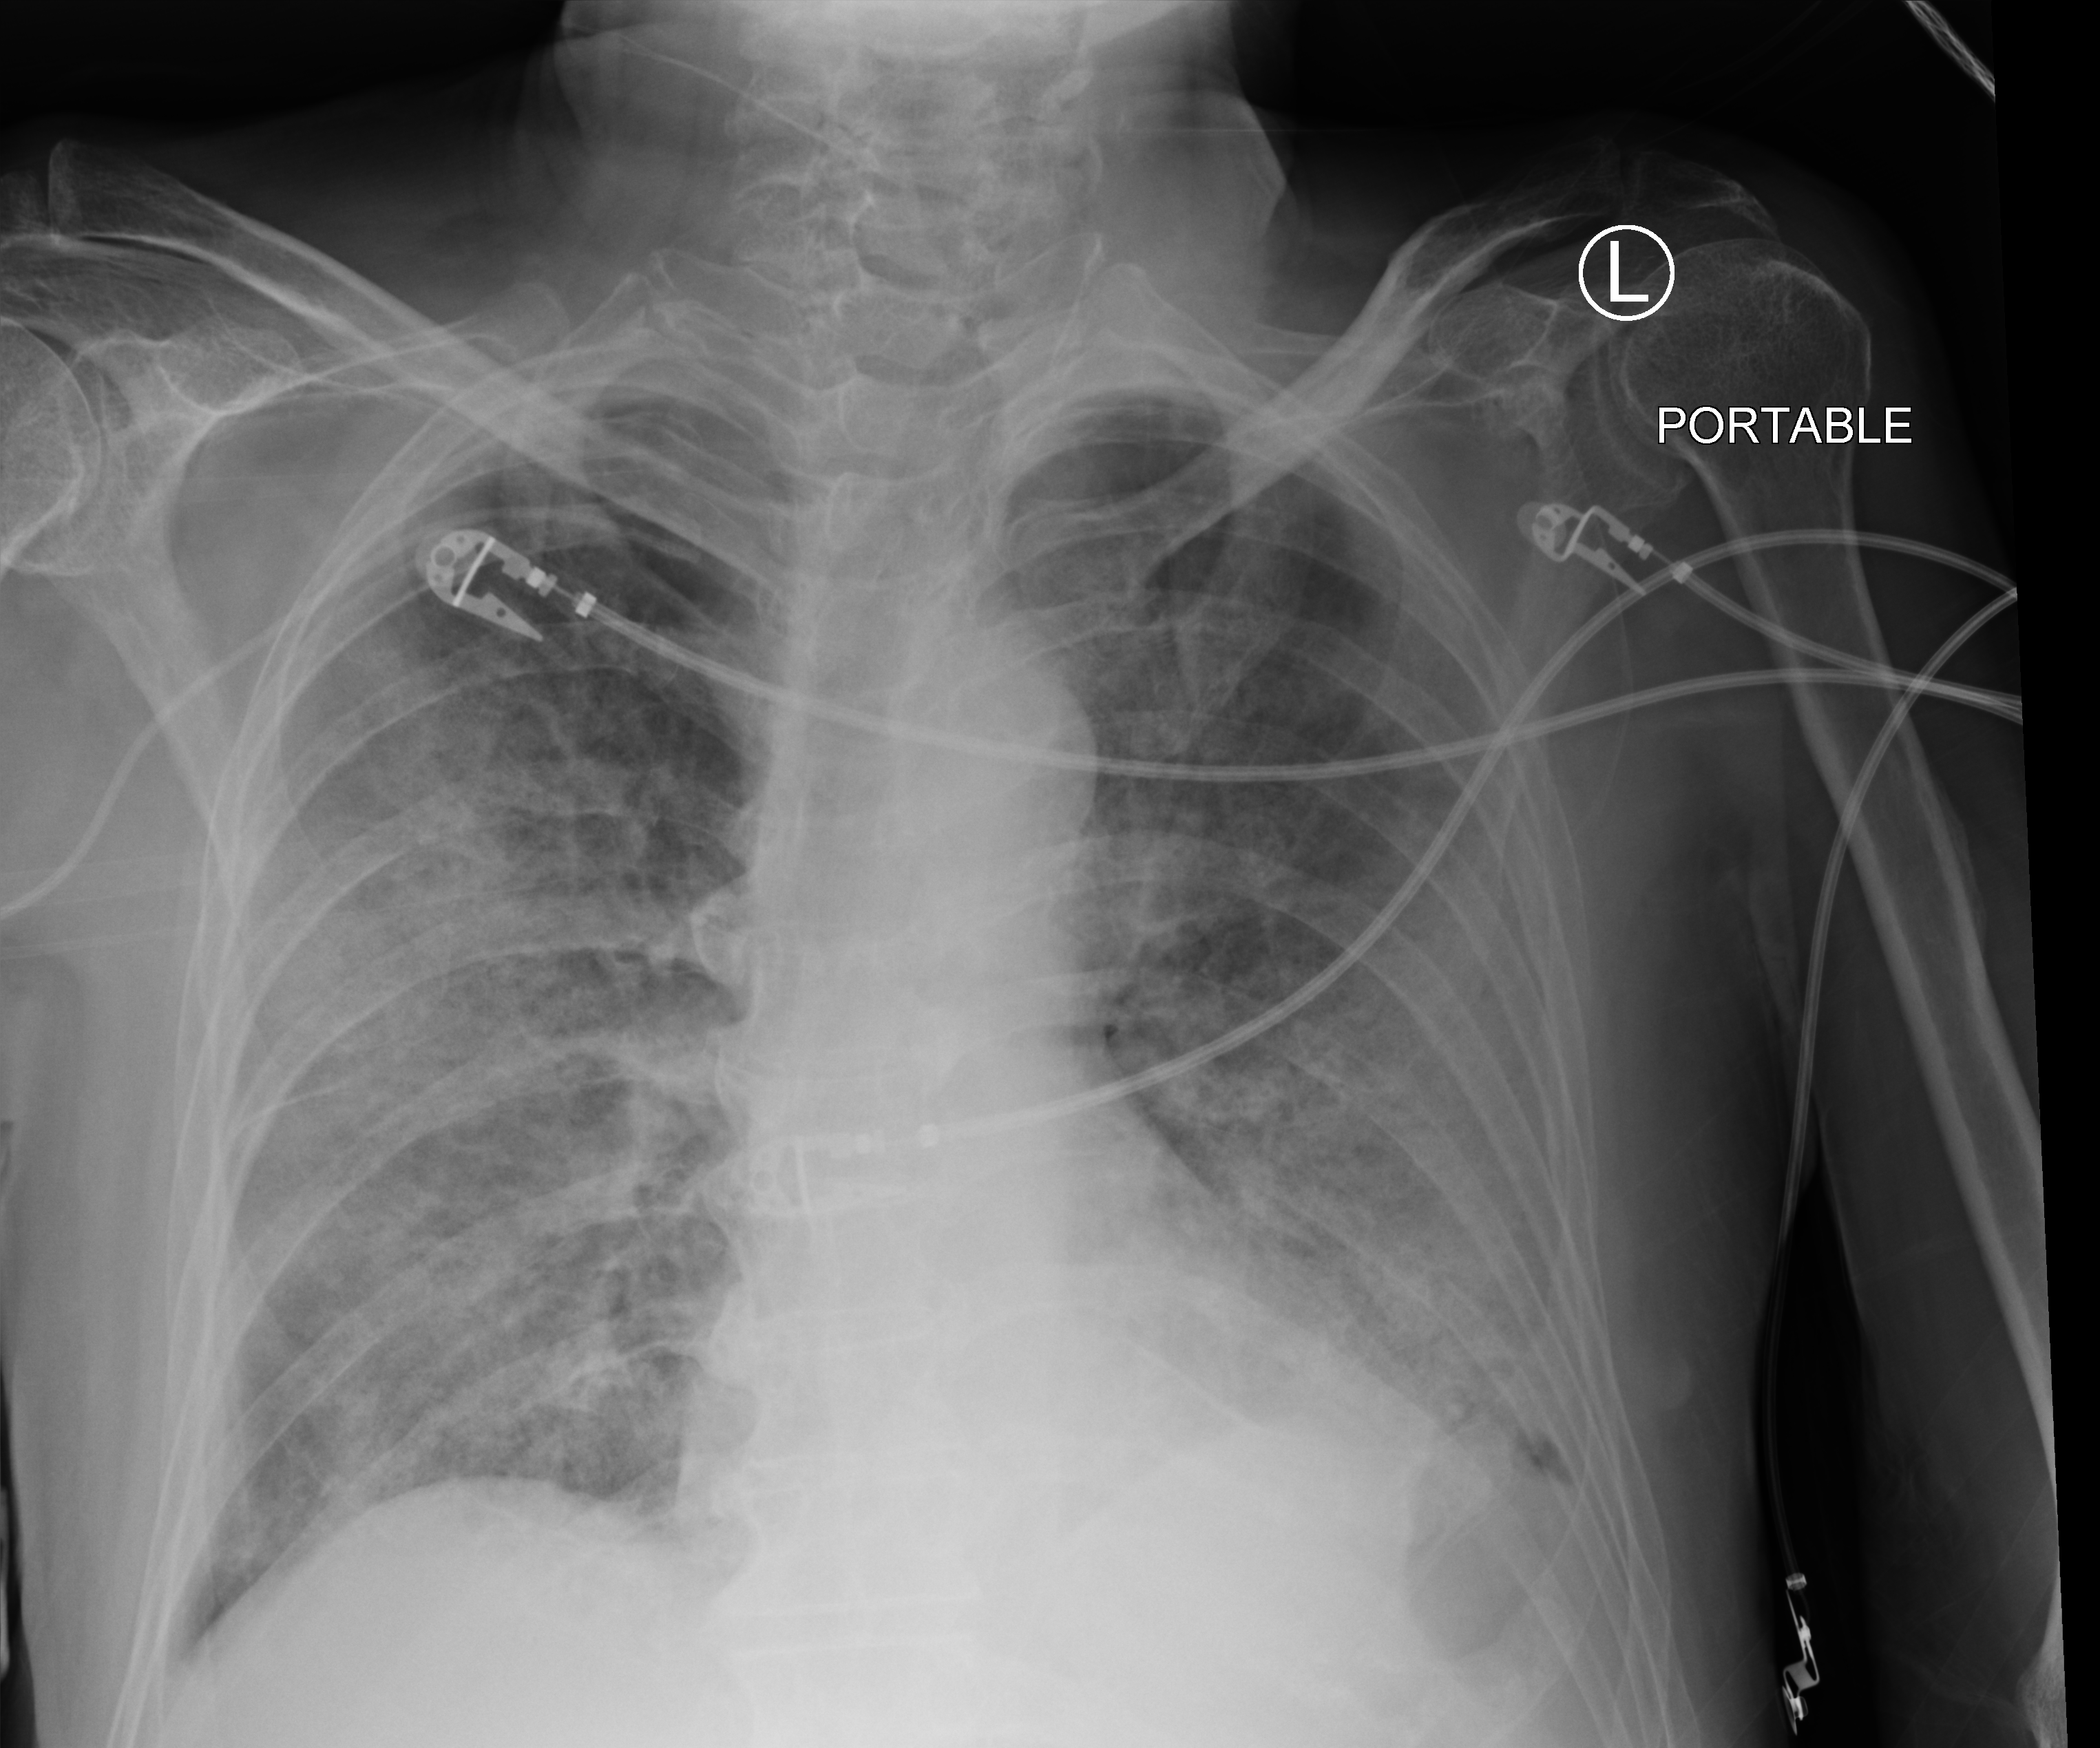
Portable chest radiograph. Male patient hospitalised with COVID-19, age 60–74 years.
From the hospital-stay record, not from the radiograph (when in the stay this image was taken is not recorded):
- mechanically ventilated during this hospital stay: yes